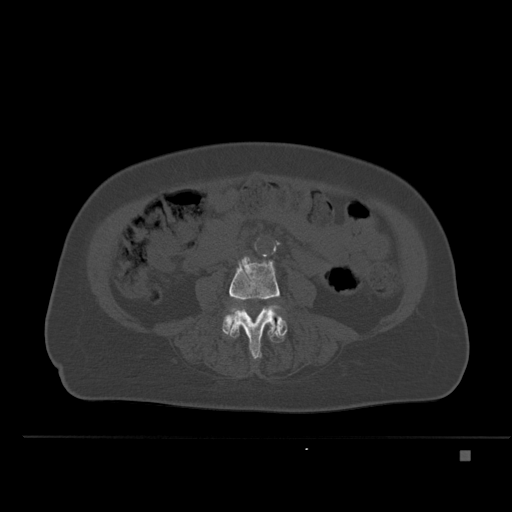
CT including the spine, one axial slice. Slice 176 of 477 in the series (ordered by position). Bone window (W 1800 / L 400 HU). 1.5 mm slice thickness. 512 × 512 image matrix, field of view 422 × 422 mm. Female patient, age 74 years. From the clinical record (not read from this slice): primary cancer: colon.
Outlined on this slice (semi-automatically segmented with operator editing):
- L4 vertebra: bounding box [x1, y1, x2, y2] px = [229, 256, 282, 359]
- L5 vertebra: [222, 311, 287, 343]